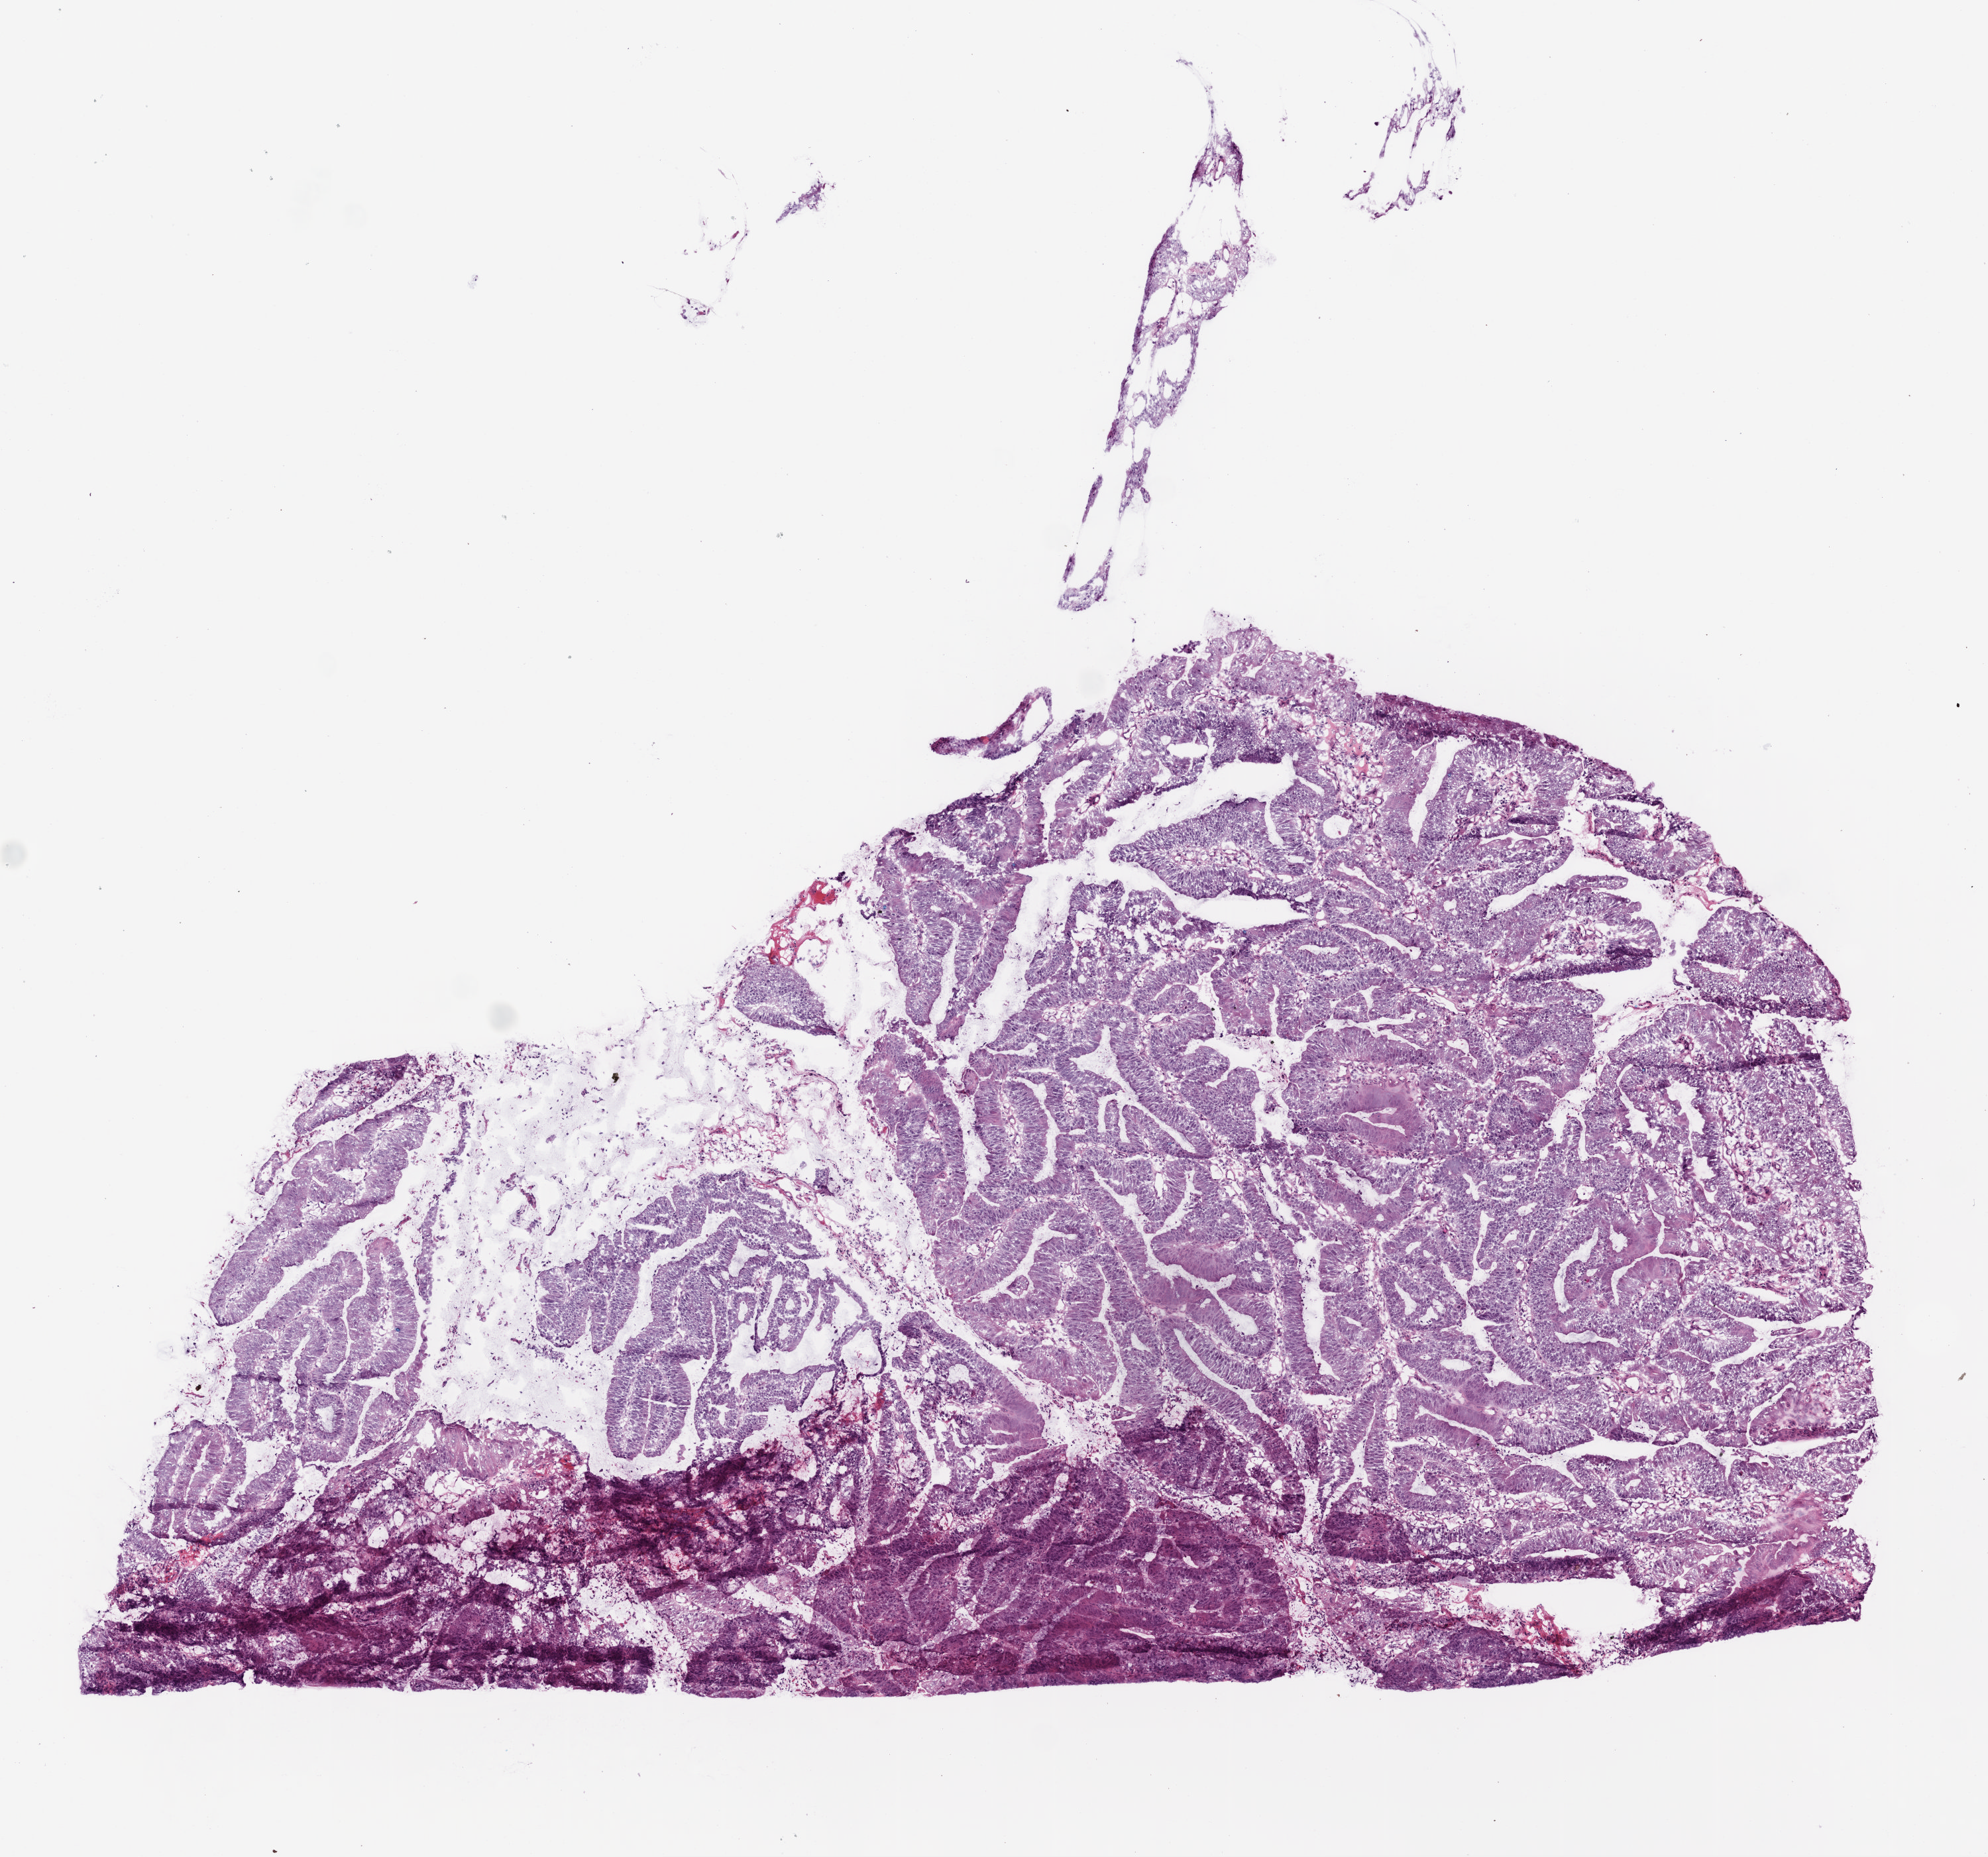
Hematoxylin and eosin (H&E) stained whole-slide image, low-resolution overview of the scanned area, about 6.0 x 5.6 mm, frozen section from the top of the tissue portion, colon, primary tumour sample. Male, age 42 years at initial diagnosis. Pathologist review of this section (percent, as recorded): tumour cells 100%, tumour nuclei 80%, normal cells 0%, stromal cells 0%, necrosis 0%.
- histologic diagnosis: Adenocarcinoma, NOS
- AJCC pathologic stage: II (5th edition)
- lymph nodes positive (case pathology): 0 of 40 examined